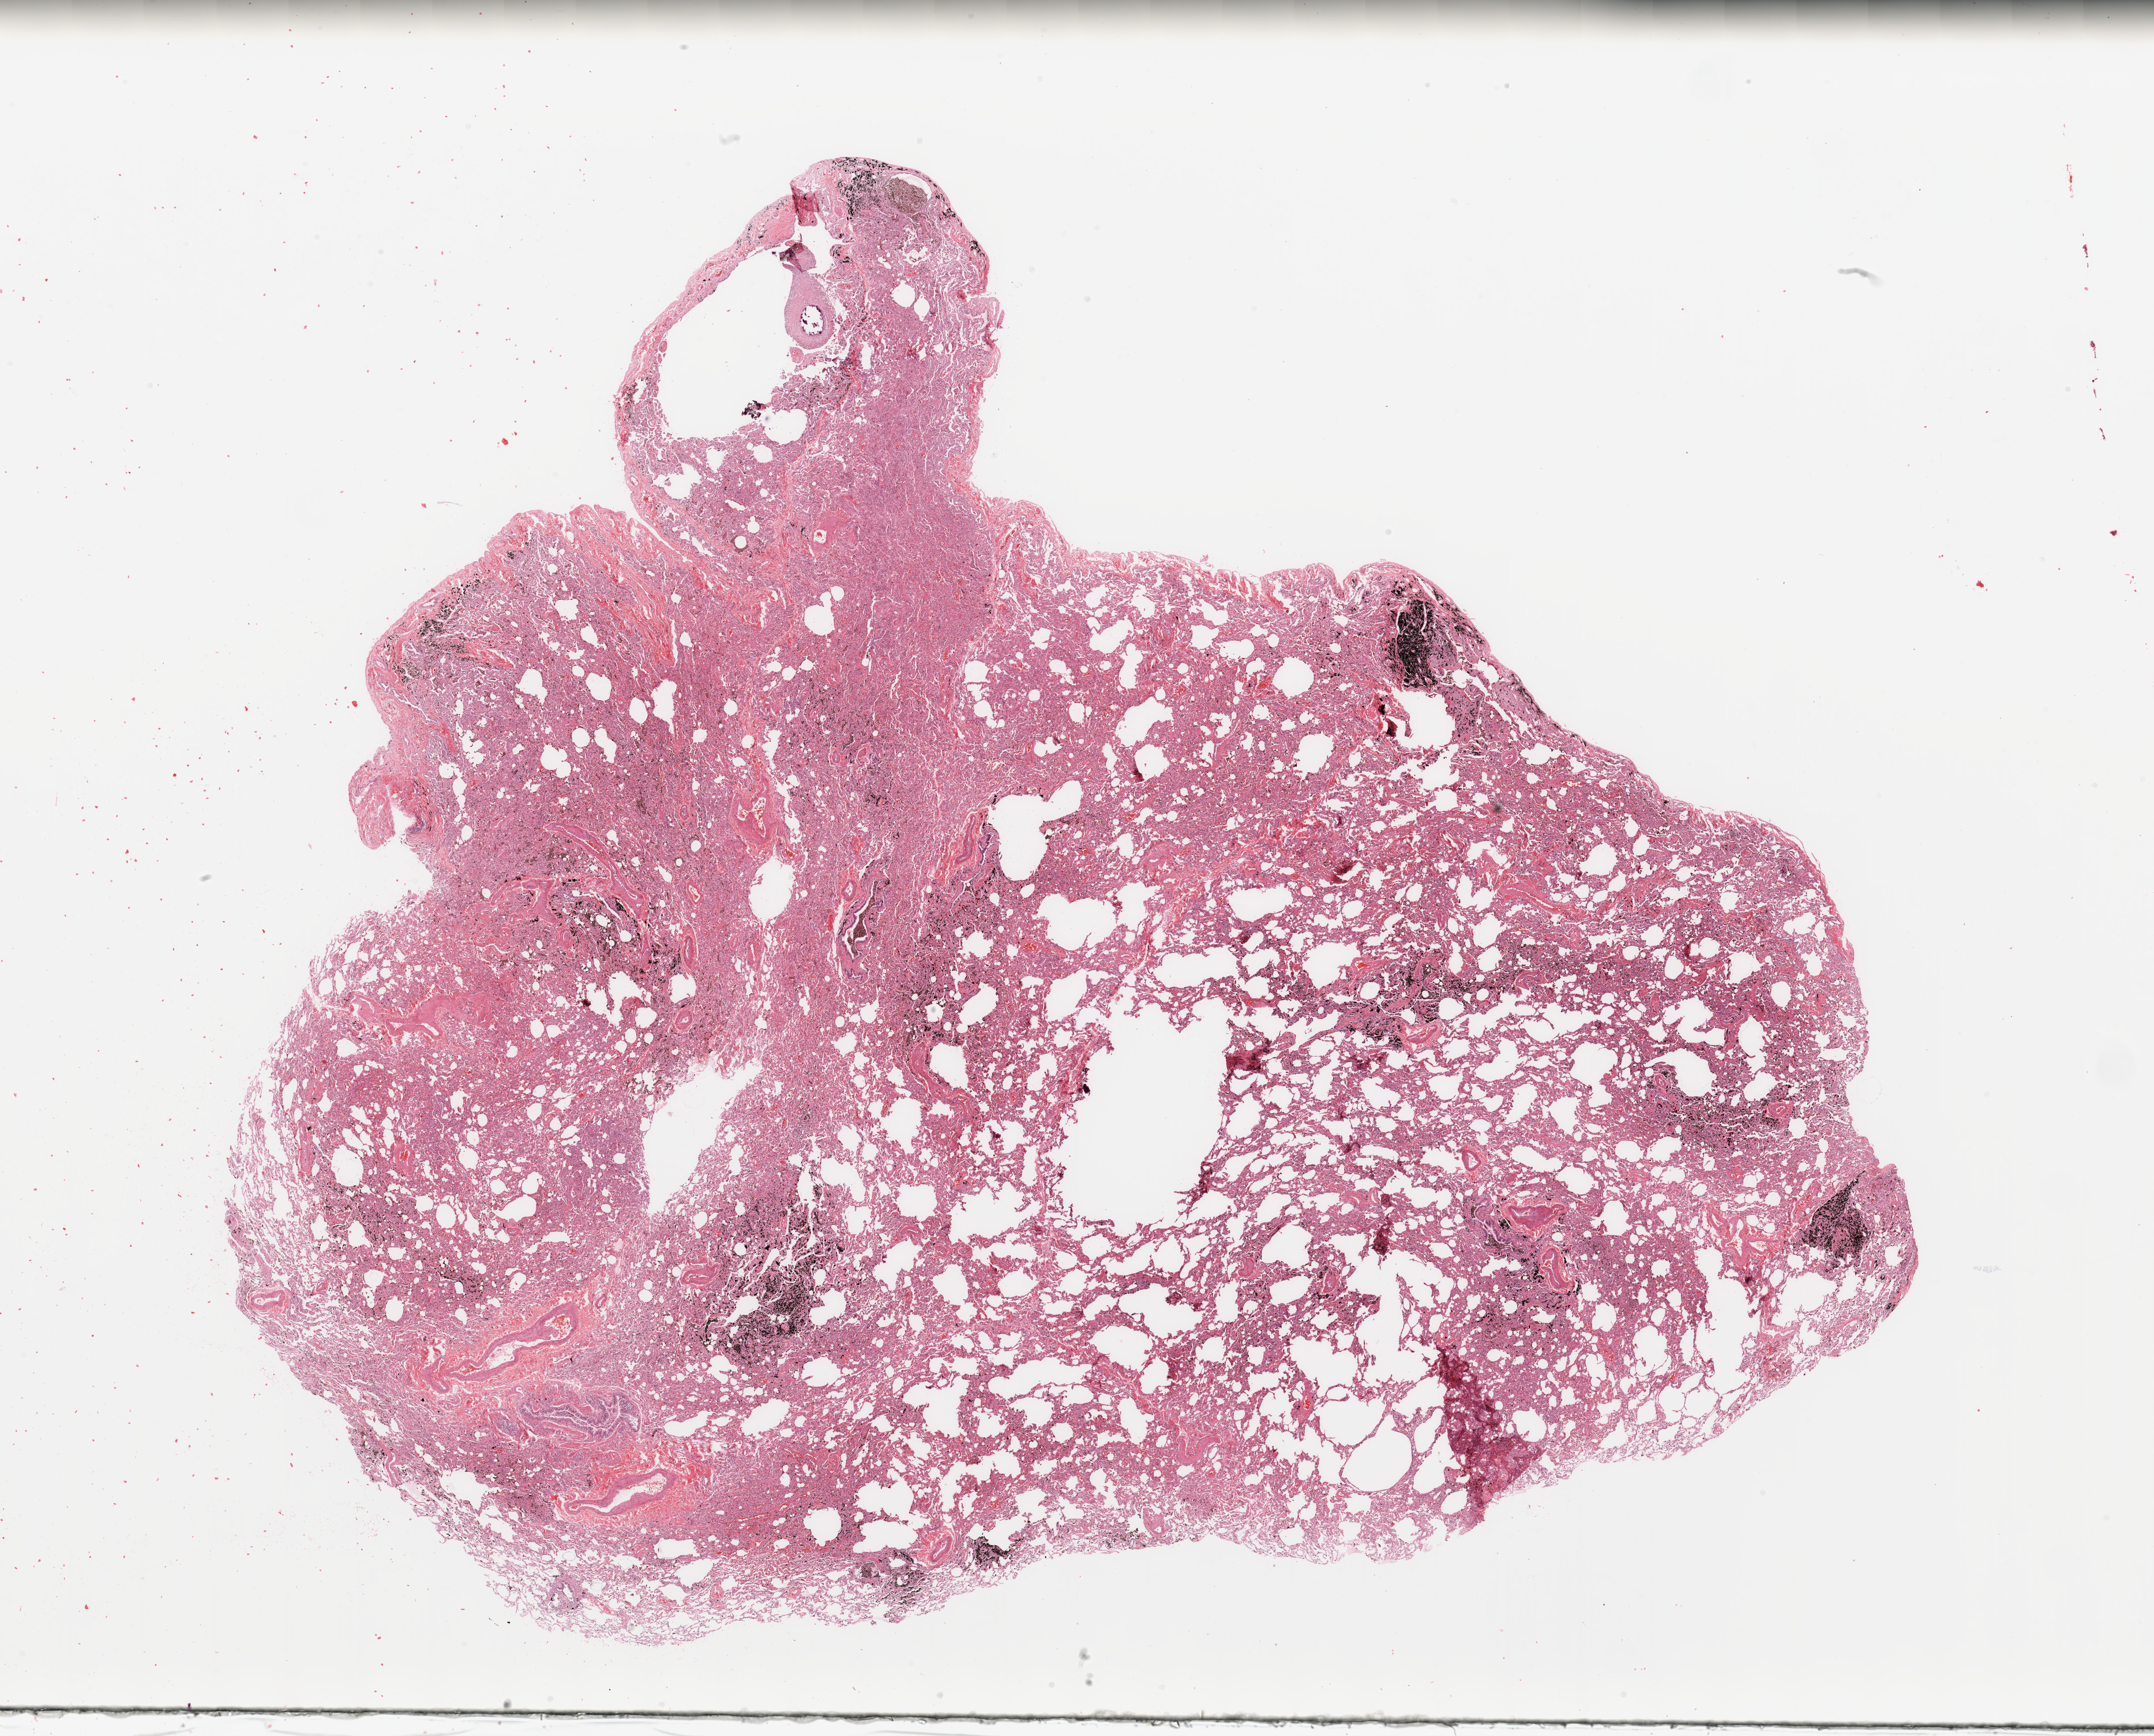
Whole-slide histology image, H&E-stained, a low-resolution overview of the entire scanned area, about 29.5 x 23.8 mm (slide scanned at 20x), lung, normal (non-tumour) tissue. 58-year-old male patient.
This section: normal (non-tumour) tissue from the same patient. Patient diagnosis: Adenocarcinoma, NOS.